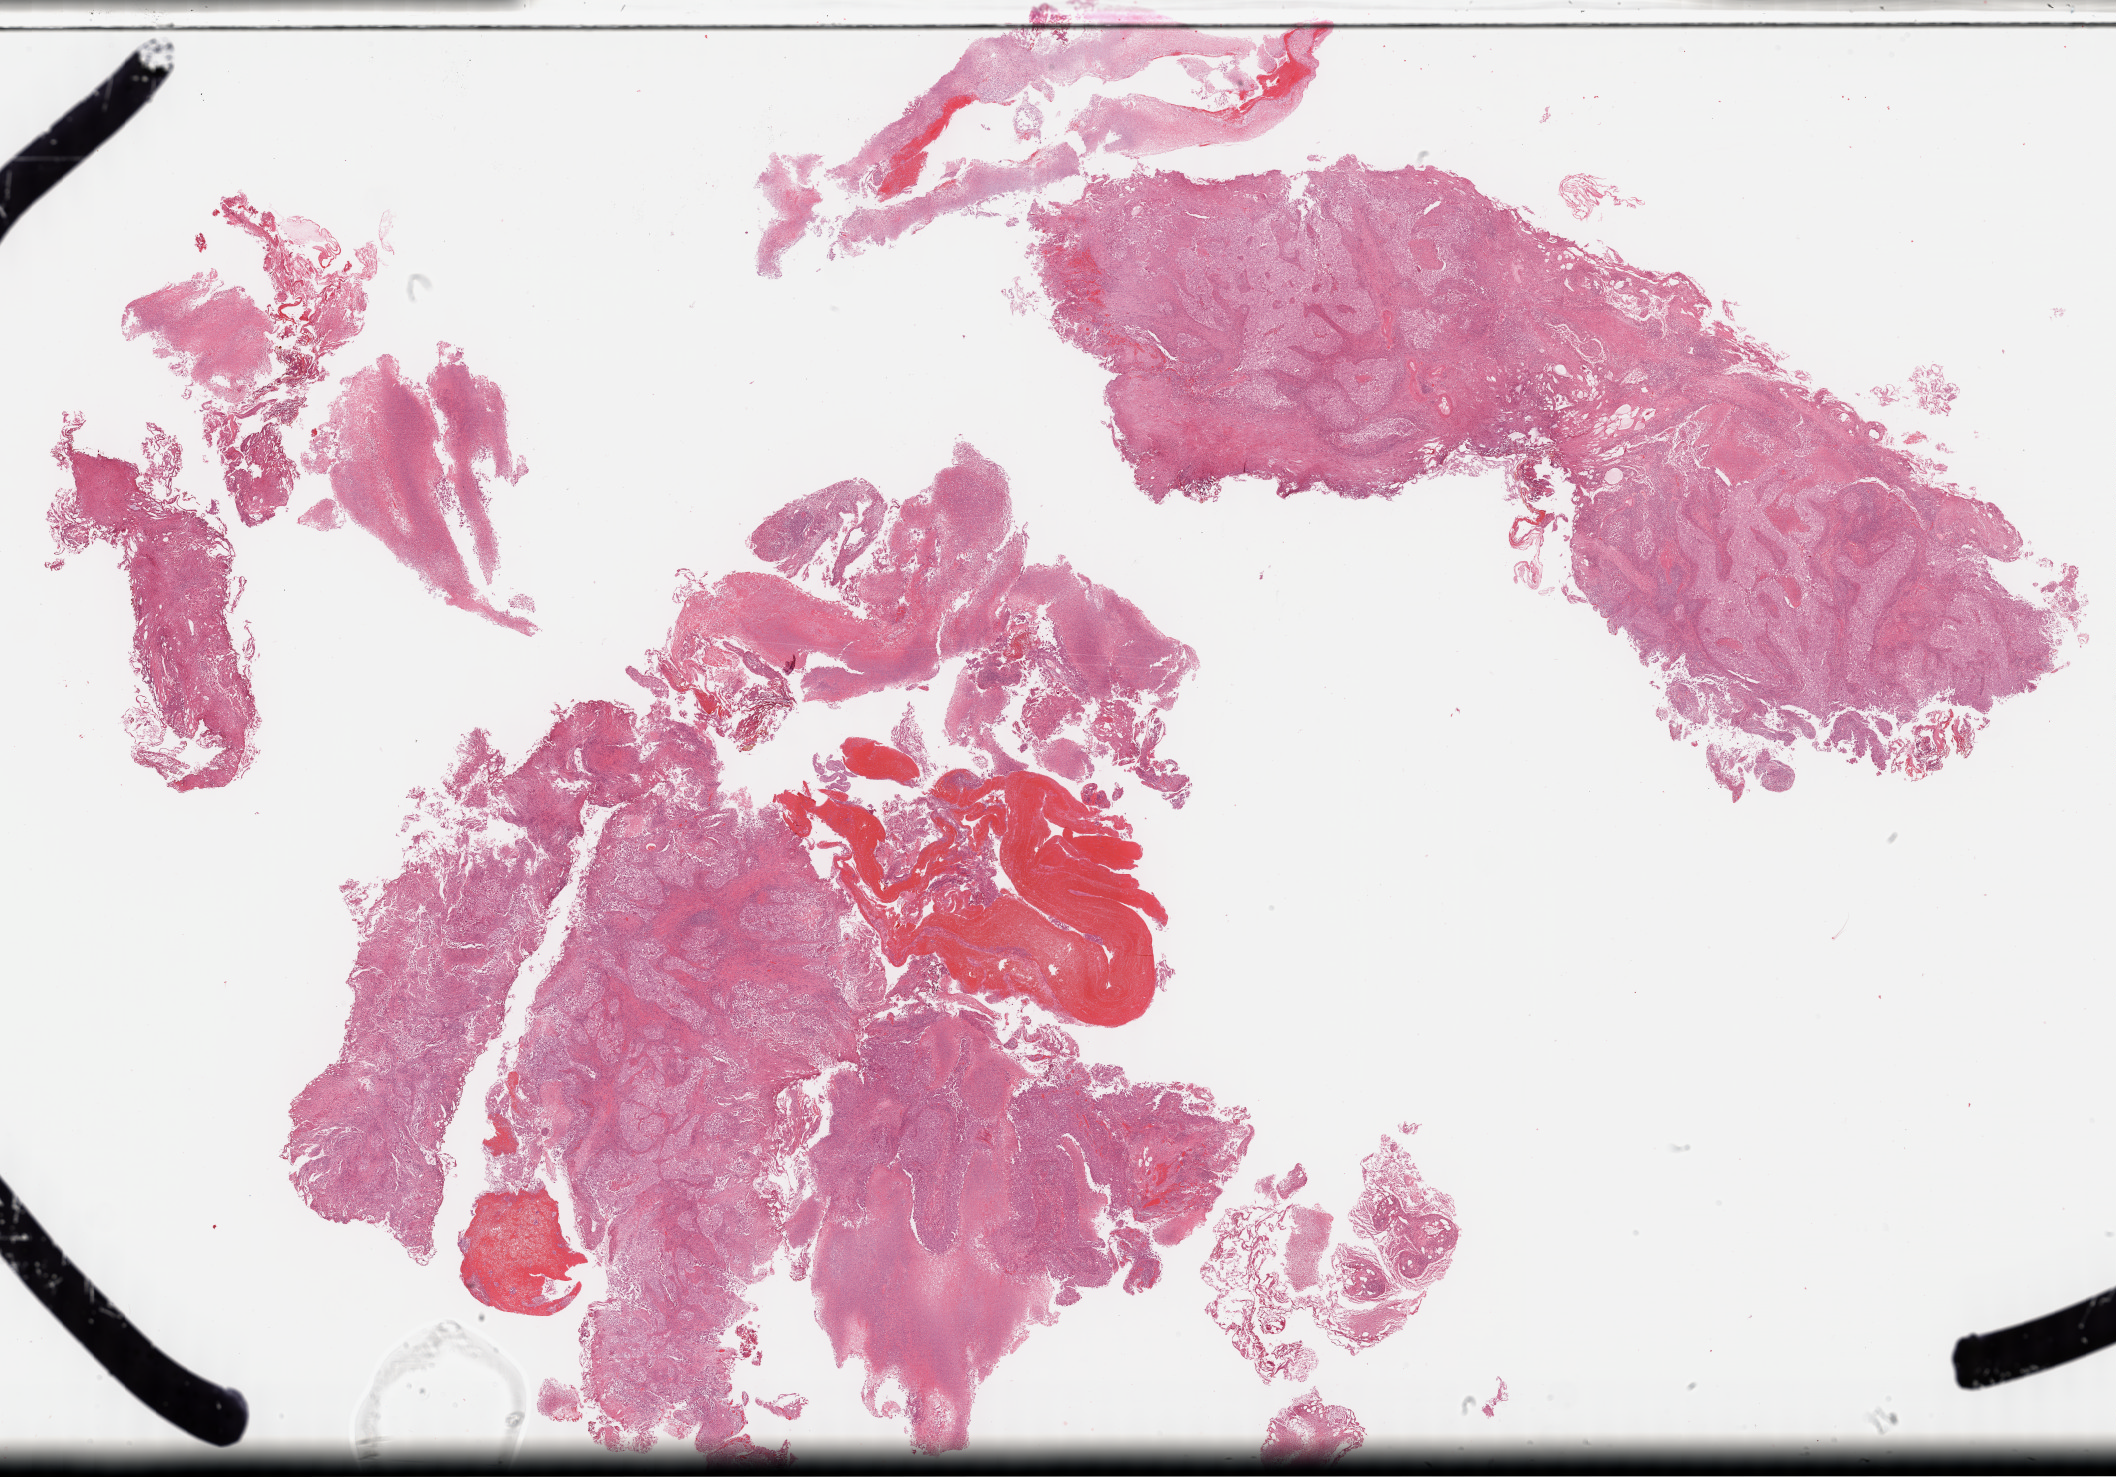
H&E whole-slide image, a low-resolution overview of the entire scanned area, about 34.2 x 23.9 mm (acquisition: 40x scan), FFPE section, primary tumour sample from the bladder. Patient: female, age at initial diagnosis 69 years. Histologic grade: high grade.
AJCC pathologic stage: II. Pathologic diagnosis: Transitional cell carcinoma.